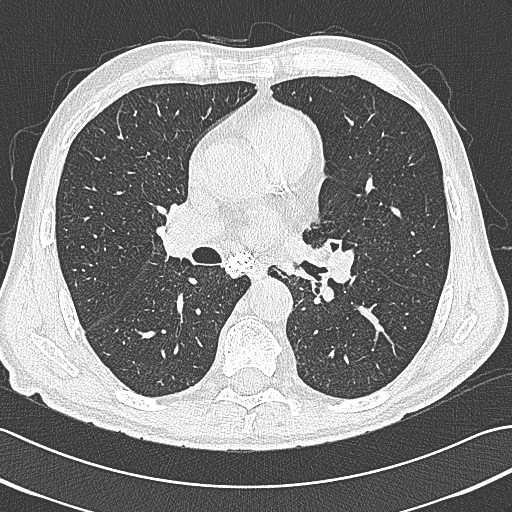
Chest CT (low-dose screening protocol), one axial image. Baseline annual screen. Lung window (W 1500 / L -600 HU). Lung (sharp) reconstruction kernel (B80f). Slice 179 of 380 in the series. Male participant, aged 65 years at enrolment. Current smoker at enrolment.
- Expert-annotated lung lesion, bounding box <304,231,351,275> (left, top, right, bottom; pixels).
- No non-calcified nodule or mass ≥4 mm was recorded by the screening reader at this exam.
- Official screen result: negative screen, minor abnormalities not suspicious for lung cancer.
- Later outcome: lung cancer diagnosed 161 days after this screen — large cell neuroendocrine carcinoma, left hilum, left main stem bronchus, stage IIIB (AJCC 6th edition), 70 mm at pathology.